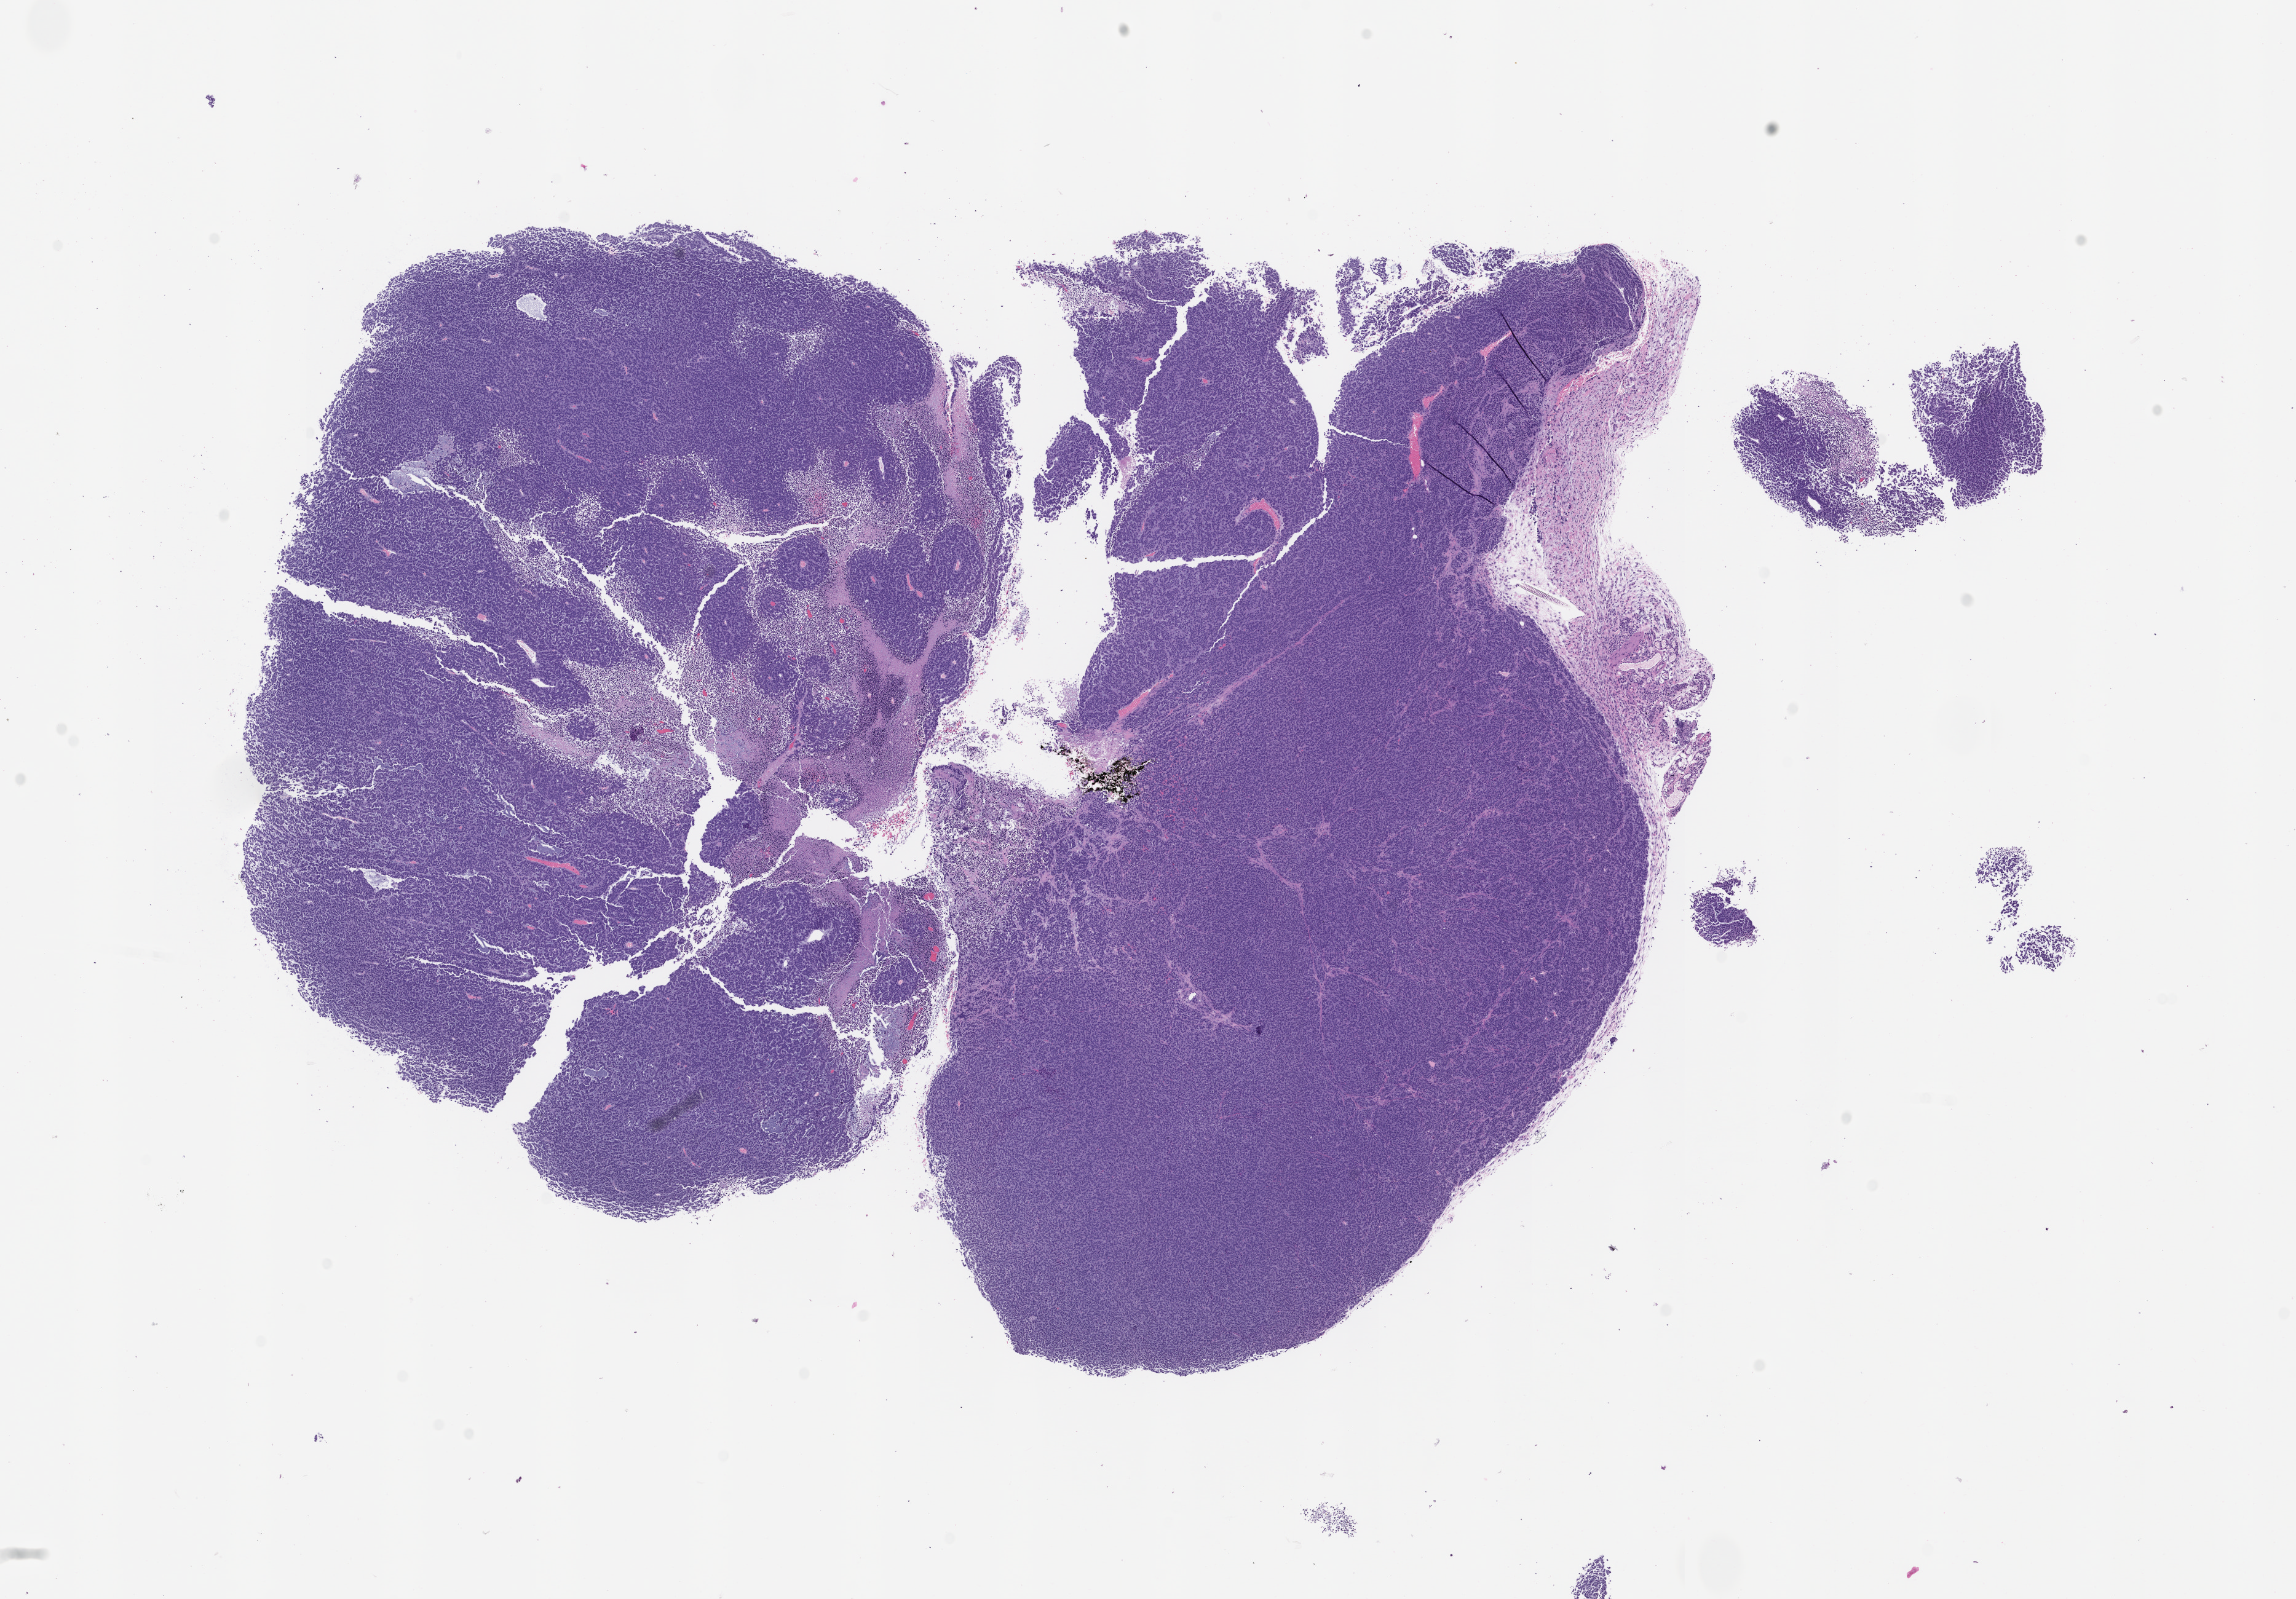
Whole-slide image, hematoxylin and eosin (H&E): patient-derived xenograft (human tumor grown in a mouse), passage 1, low-resolution overview of the scanned area, about 15.0 x 10.4 mm. FFPE section. Originating tumor site category: ovary.
Originating patient diagnosis: Ovarian Carcinoma.